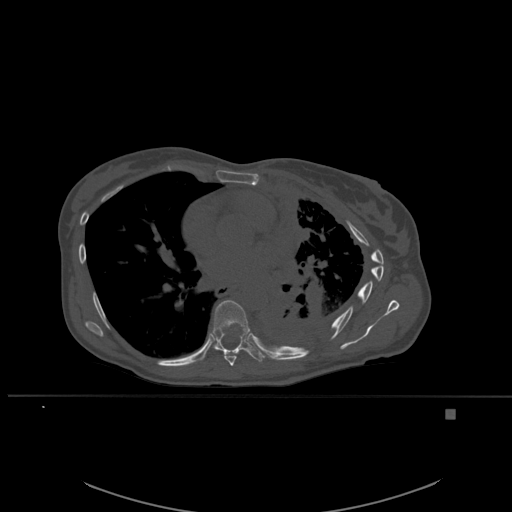
CT including the spine, one axial slice; position 357 of 537 along the scan axis; bone window (W 1800 / L 400 HU); 512 × 512 image matrix. Patient: female, 45 years. From the clinical record (not read from this slice): primary cancer: lung.
Structures marked on this image (semi-automatically segmented with operator editing):
- T7 vertebra: box from (x=220, y=350) to (x=244, y=366) px
- T8 vertebra: (x=212, y=300)–(x=263, y=362)